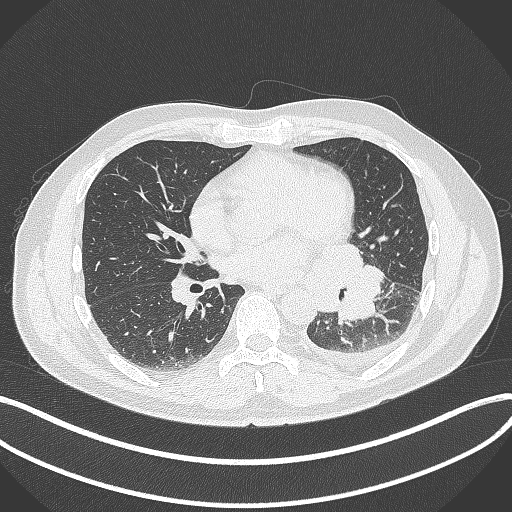
Chest CT, one axial slice; position 167 of 342 along the scan axis; reconstruction kernel B70f; lung window (W 1500 / L -600 HU); 1 mm slice thickness; 512 × 512 image matrix, field of view 400 × 400 mm. Male patient, age 58 years. Case-level facts recorded for this patient, not image findings: clinical TNM (as recorded): T3 N1 M1b; histopathological grade: G3.
Outlined on this slice (bounding box drawn by a radiologist):
- lung tumour (recorded histology: small cell carcinoma): bounding box <309,238,385,325> (left, top, right, bottom; pixels)